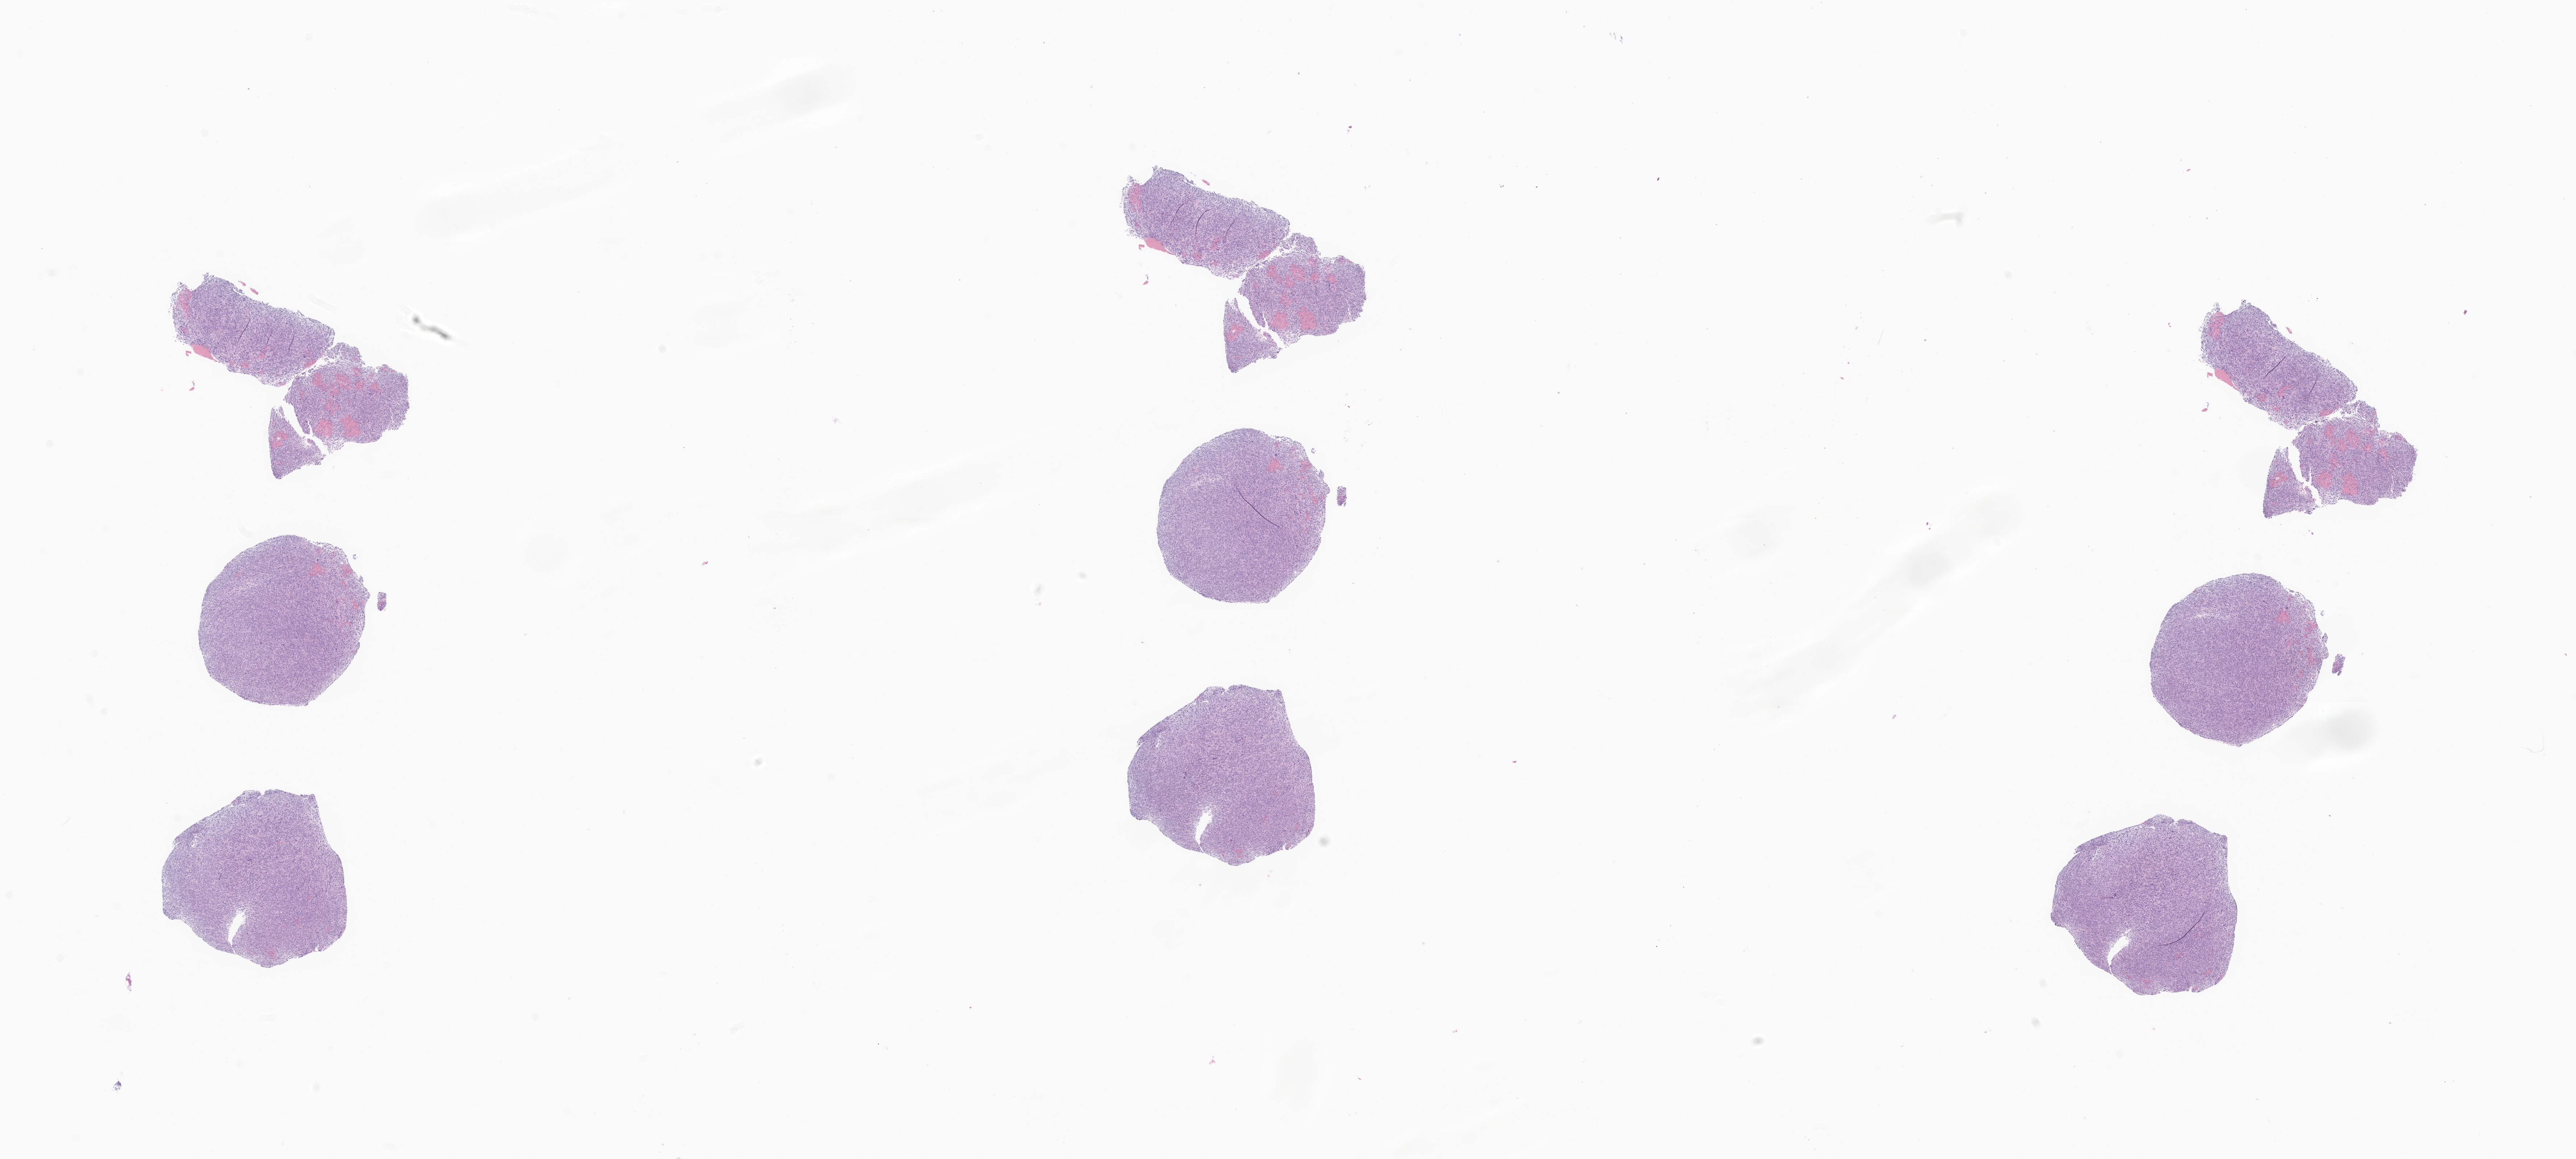
Whole-slide image, hematoxylin and eosin (H&E) stain of tumor tissue from the brain, a low-resolution overview of the entire scanned area, about 29.9 x 13.5 mm; formalin-fixed paraffin-embedded section. Patient: male, age 76 months (6 years 4 months).
Recorded diagnosis: Glioma, malignant.